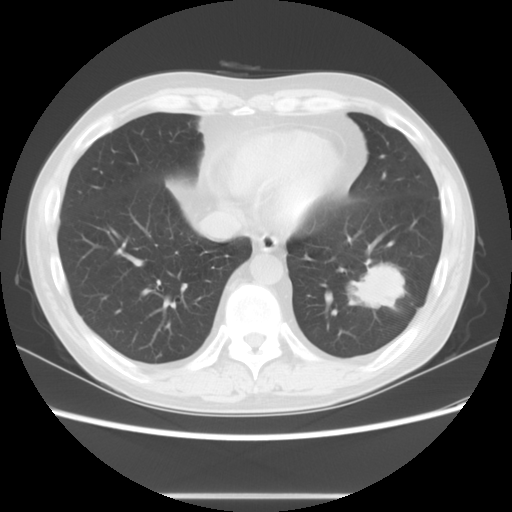
Chest CT, one axial slice; slice 24 of 63 in the series (ordered by position); lung window (W 1500 / L -600 HU); 5 mm slice thickness; 512 × 512 image matrix, field of view 347 × 347 mm. Patient: male, 49 years. From the clinical record (not read from this slice): clinical TNM (as recorded): T3 N0 M0; histopathological grade: G2-3.
Structures marked on this image (rectangle marked by the reading radiologist):
- lung tumour (recorded histology: squamous cell carcinoma): bounding box (x1, y1, x2, y2) in pixels: (344, 256, 416, 319)